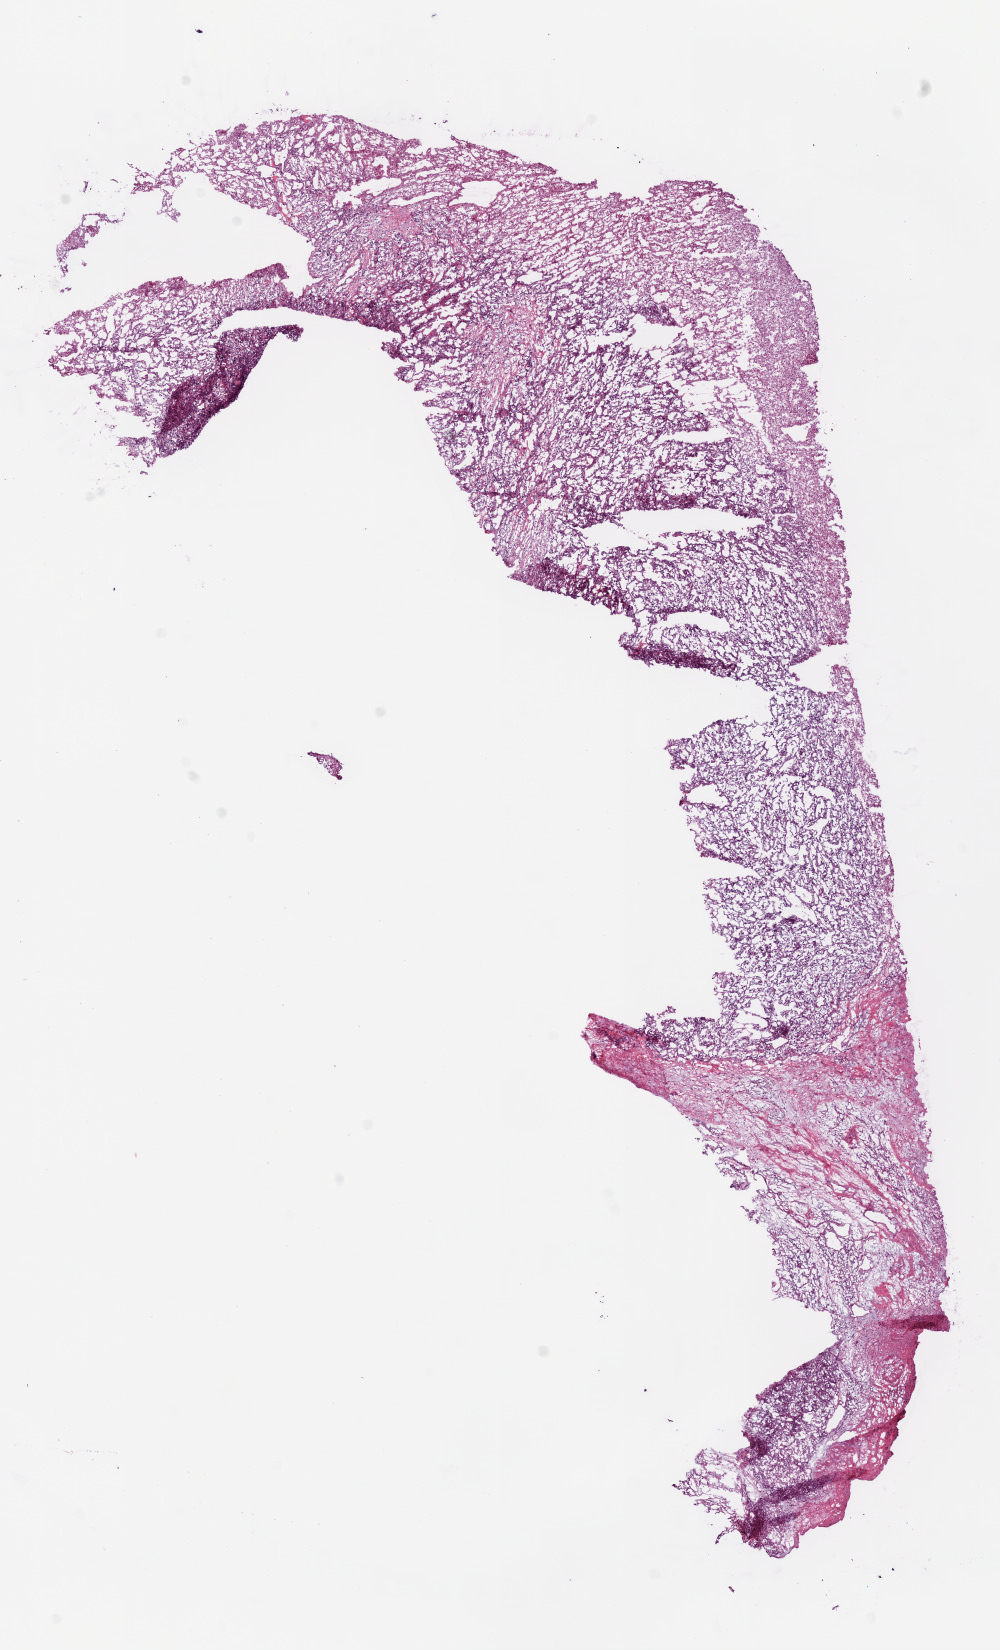
Whole-slide histology image, H&E — whole scanned area (about 8.0 x 13.2 mm, from a 20x scan) shown as a low-resolution overview. Frozen section from the bottom of the tissue portion. Primary tumour sample from the kidney. Male, age 69 years at initial diagnosis. Histologic grade: G3 (poorly differentiated). Slide review estimates, as recorded: tumour cells 85%, tumour nuclei 75%, normal cells 0%, stromal cells 15%, necrosis 0%.
AJCC pathologic stage: III. Laterality: left. TNM: T3a NX M0. Diagnosis: Clear cell adenocarcinoma, NOS.